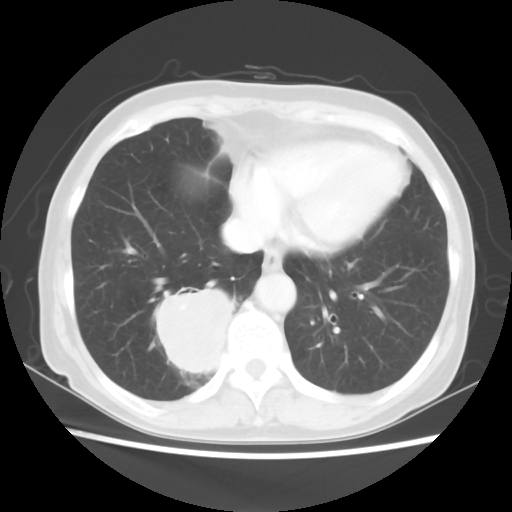
Chest CT, one axial slice. Slice 17 of 56 in the series (ordered by position). 120 kVp. Lung window (W 1500 / L -600 HU). 5 mm slice thickness. 512 × 512 image matrix, field of view 332 × 332 mm. Patient: female, 66 years. From the clinical record (not read from this slice): clinical TNM (as recorded): T2 N3 M0; histopathological grade: G3.
Outlined on this slice (bounding box drawn by a radiologist):
- lung tumour (recorded histology: small cell carcinoma): box from (x=143, y=279) to (x=234, y=383) px